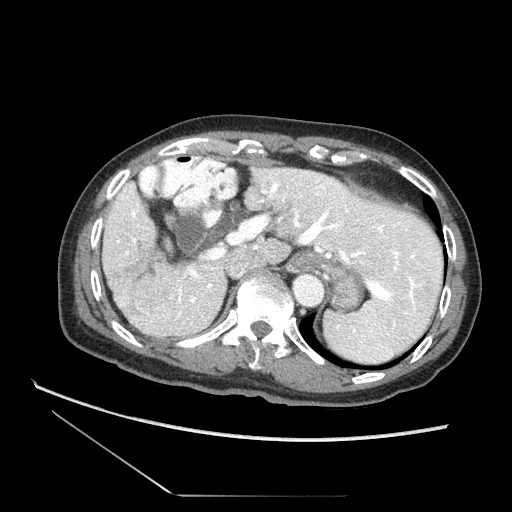
Contrast-enhanced abdominal CT (liver protocol), one axial slice. Slice 56 of 73 in the series (ordered by position). Reconstruction kernel STANDARD. Soft-tissue window (W 400 / L 40 HU). 512 × 512 image matrix, field of view 360 × 360 mm. From the clinical record (not read from this slice): diagnosis: hepatocellular carcinoma (patient treated with transarterial chemoembolisation; whether this scan precedes or follows treatment is not stated here); TNM stage (as recorded): Stage-II; Child-Pugh class: A; tumour differentiation: moderately differentiated.
Outlined on this slice (semi-automatic segmentation, software-assisted and operator-edited):
- liver parenchyma outside the tumour (the mass and vessels are separate outlines, so this box may not span the whole liver): box from (x=104, y=165) to (x=447, y=353) px
- mass: (x=128, y=272)–(x=180, y=316)
- liver vessels: (x=133, y=185)–(x=427, y=310)